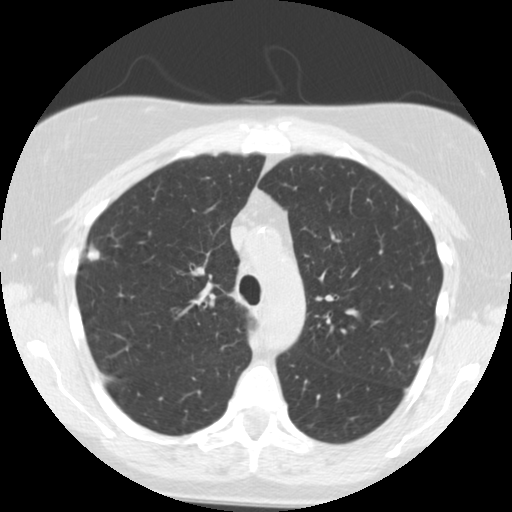
Axial slice from a low-dose chest CT screening exam; second annual screen; lung window (W 1500 / L -600 HU); 120 kVp; slice 170 of 244 in the series; 512 × 512 image matrix. Female, age 55 years at enrolment. Current smoker at enrolment.
- Expert-annotated lung lesion, bounding box <69,238,115,276> (left, top, right, bottom; pixels).
- No non-calcified nodule or mass ≥4 mm was recorded by the screening reader at this exam.
- Official screen result: negative screen, minor abnormalities not suspicious for lung cancer.
- Participant outcome: lung cancer diagnosed 621 days after this screen (after the third annual screen) — bronchiolo-alveolar adenocarcinoma, NOS, right upper lobe, moderately differentiated (G2), stage IIA (AJCC 6th edition), 13 mm at pathology.